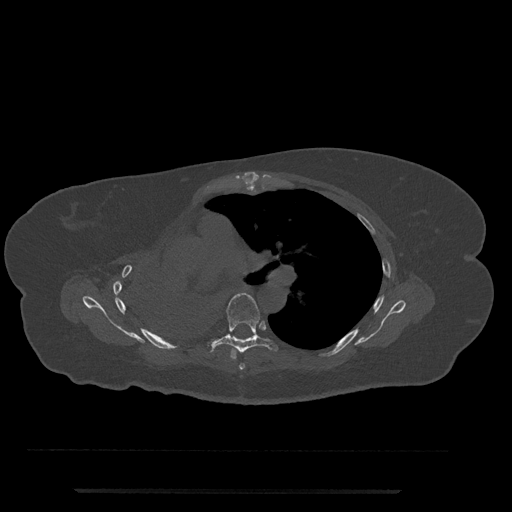
CT including the spine, one axial slice. Position 499 of 797 along the scan axis. Reconstruction kernel Br40s/3. 120 kVp. Bone window (W 1800 / L 400 HU). 512 × 512 image matrix, field of view 440 × 440 mm. Female patient, age 51 years. From the clinical record (not read from this slice): primary cancer: neuro; vertebrae with lytic lesions (as recorded): T8.
Outlined on this slice (semi-automatically segmented with operator editing):
- T5 vertebra: bounding box [x1, y1, x2, y2] px = [239, 363, 245, 370]
- T6 vertebra: [207, 293, 278, 359]